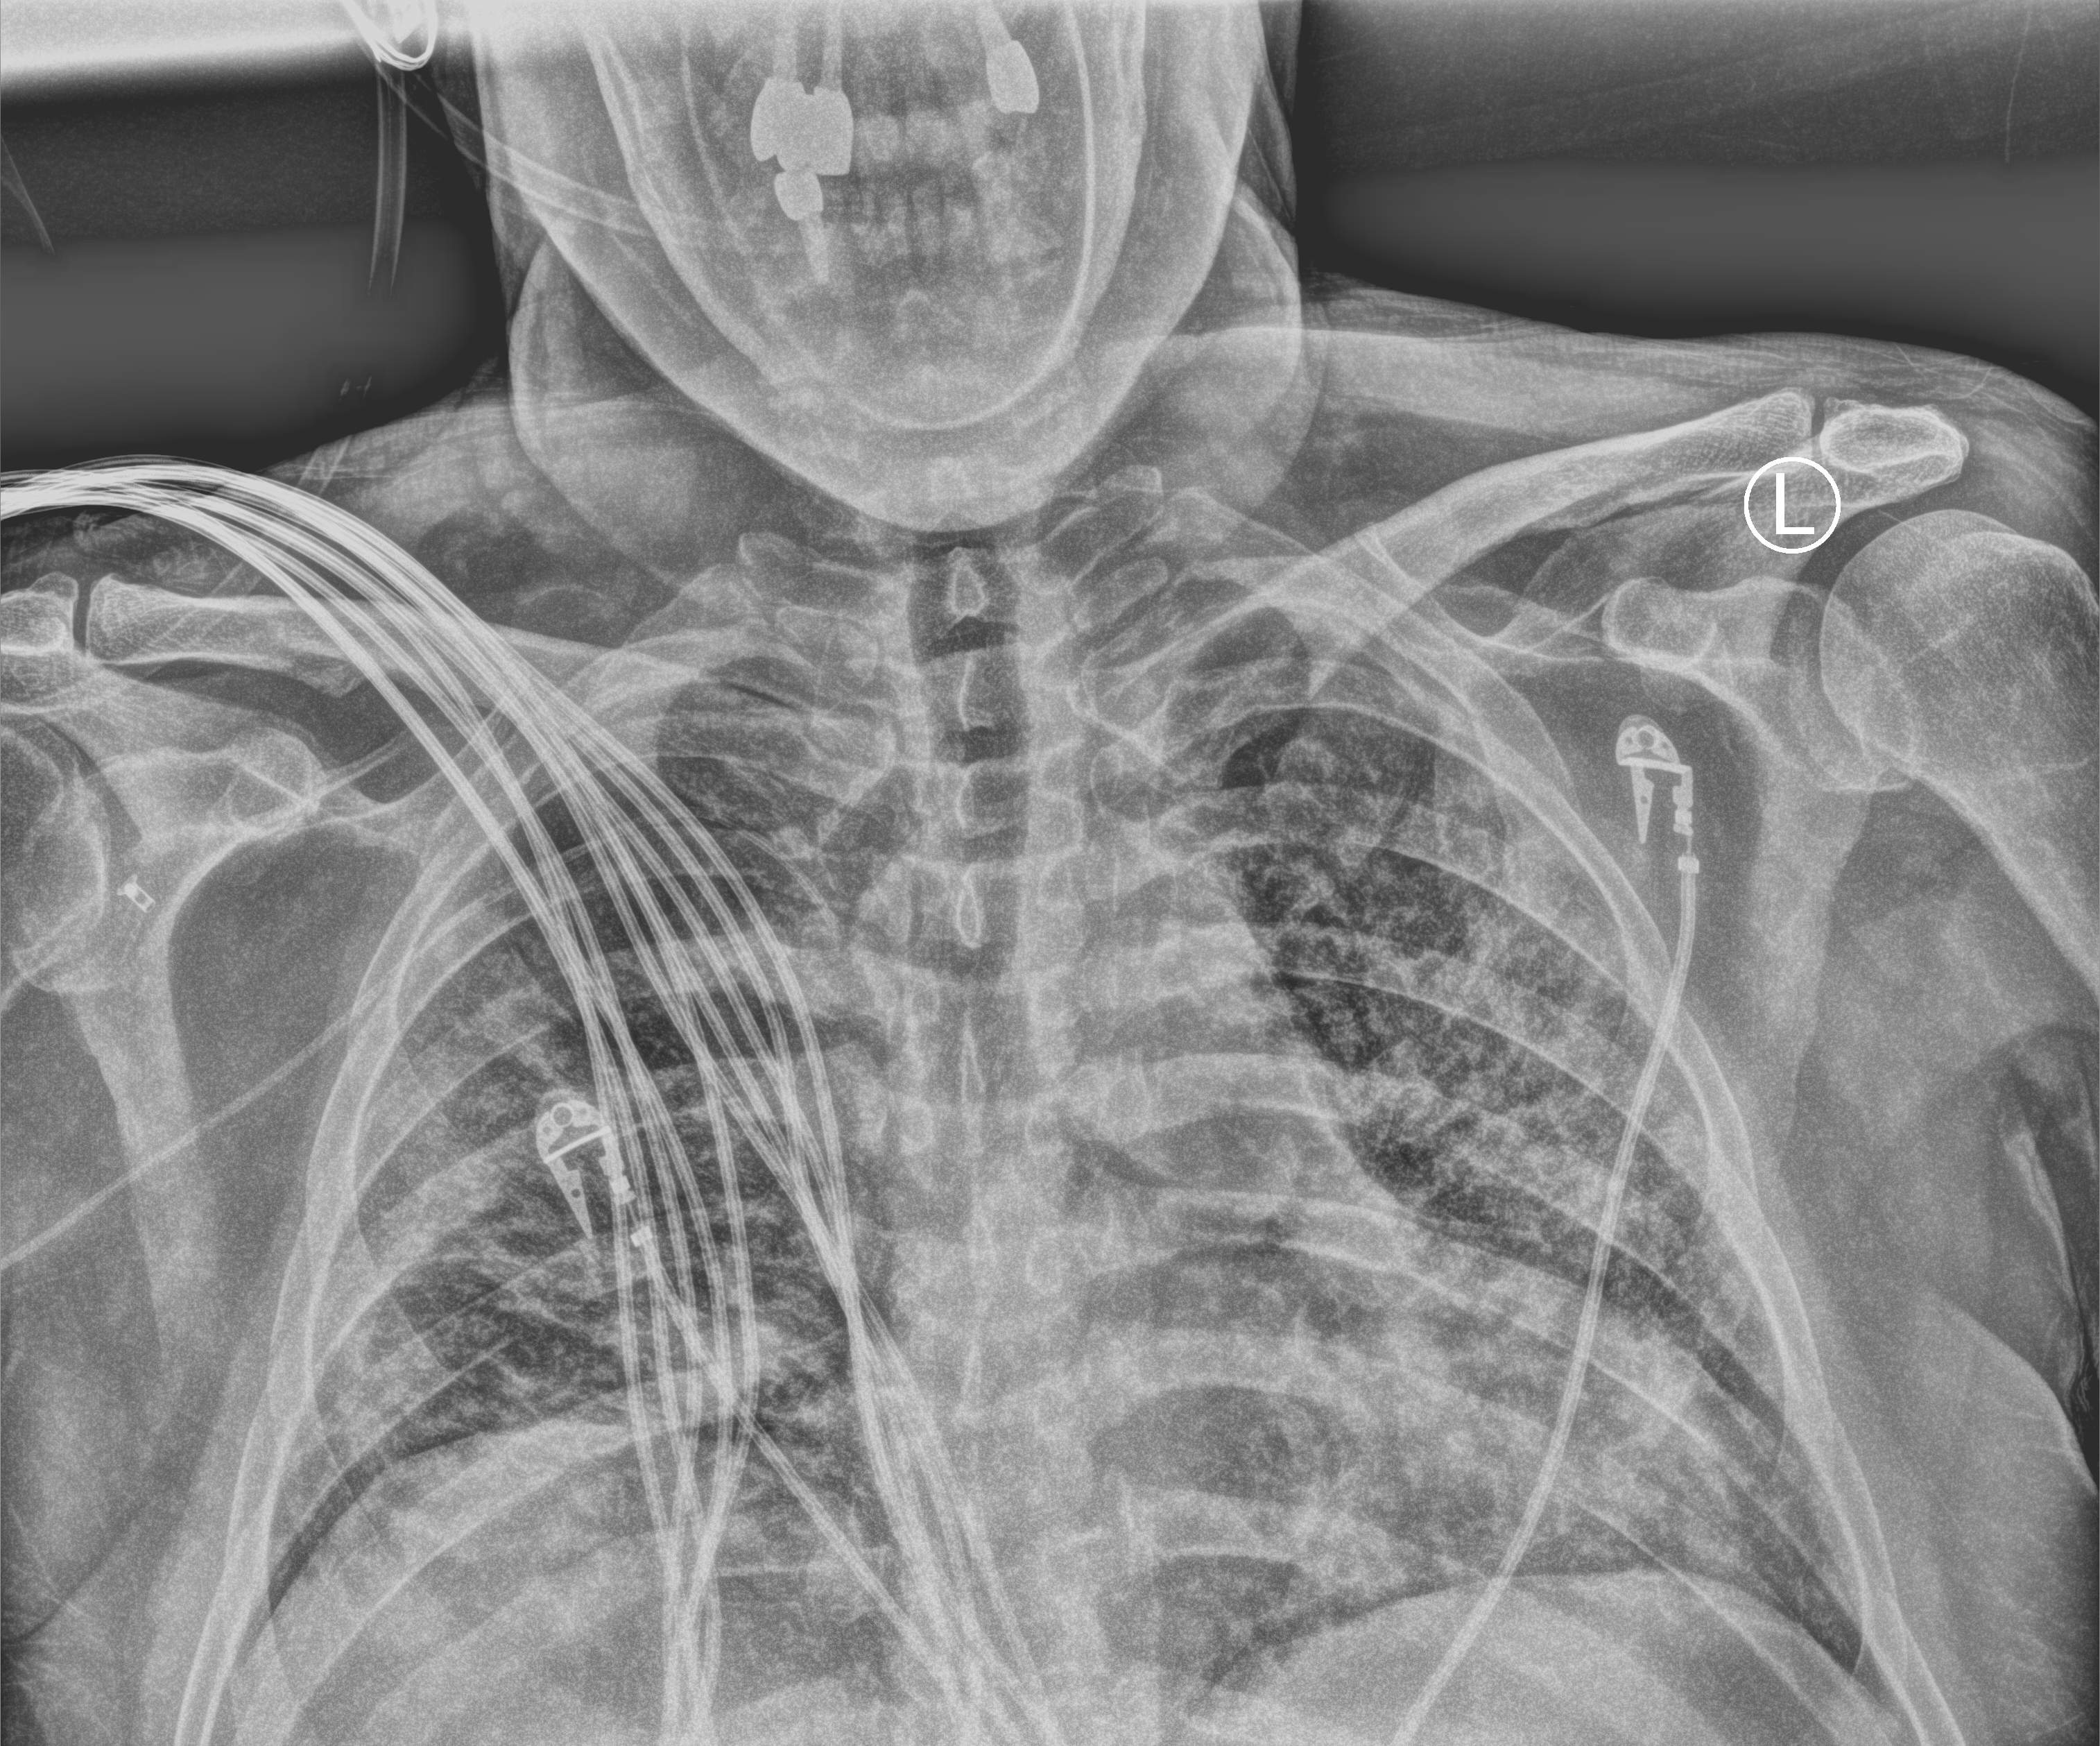
Portable chest radiograph. Male patient hospitalised with COVID-19, age 18–59 years.
From the hospital-stay record, not from the radiograph (when in the stay this image was taken is not recorded): mechanically ventilated during this hospital stay: yes; length of hospital stay: 52 days; chronic kidney disease (admission record): no.